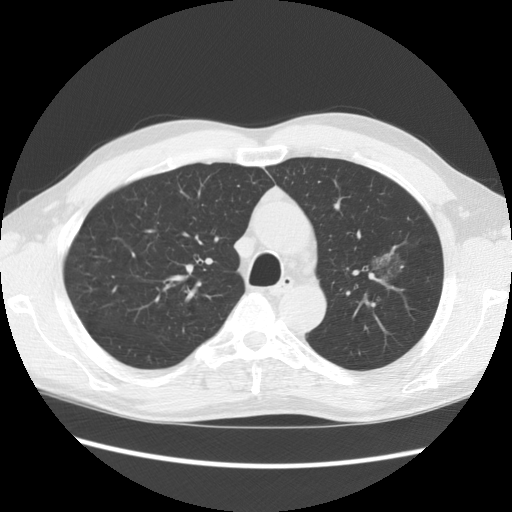
Low-dose screening chest CT, axial slice. Second annual screen. Lung window (W 1500 / L -600 HU). 2.5 mm slice thickness. Standard (soft-tissue) reconstruction kernel (STANDARD). 512 × 512 image matrix, field of view 360 × 360 mm. Male participant, aged 61 years at enrolment. Former smoker at enrolment.
- Lesion marked by an expert reader, bounding box <348,225,422,298> (left, top, right, bottom; pixels).
- Reader record for this screening exam (exam-level; its link to the box is not recorded): non-calcified nodule or mass ≥4 mm, left upper lobe, 34 × 32 mm, poorly defined margins, mixed attenuation, pre-existing on the prior screen: yes; interval growth: no.
- Official screen result: positive, no significant change: stable abnormalities potentially related to lung cancer, unchanged since the prior screening exam.
- Later outcome: lung cancer diagnosed 704 days after this screen (after the third annual screen) — bronchiolo-alveolar adenocarcinoma, NOS, left upper lobe, well differentiated (G1), stage IB (AJCC 6th edition), 44 mm at pathology.